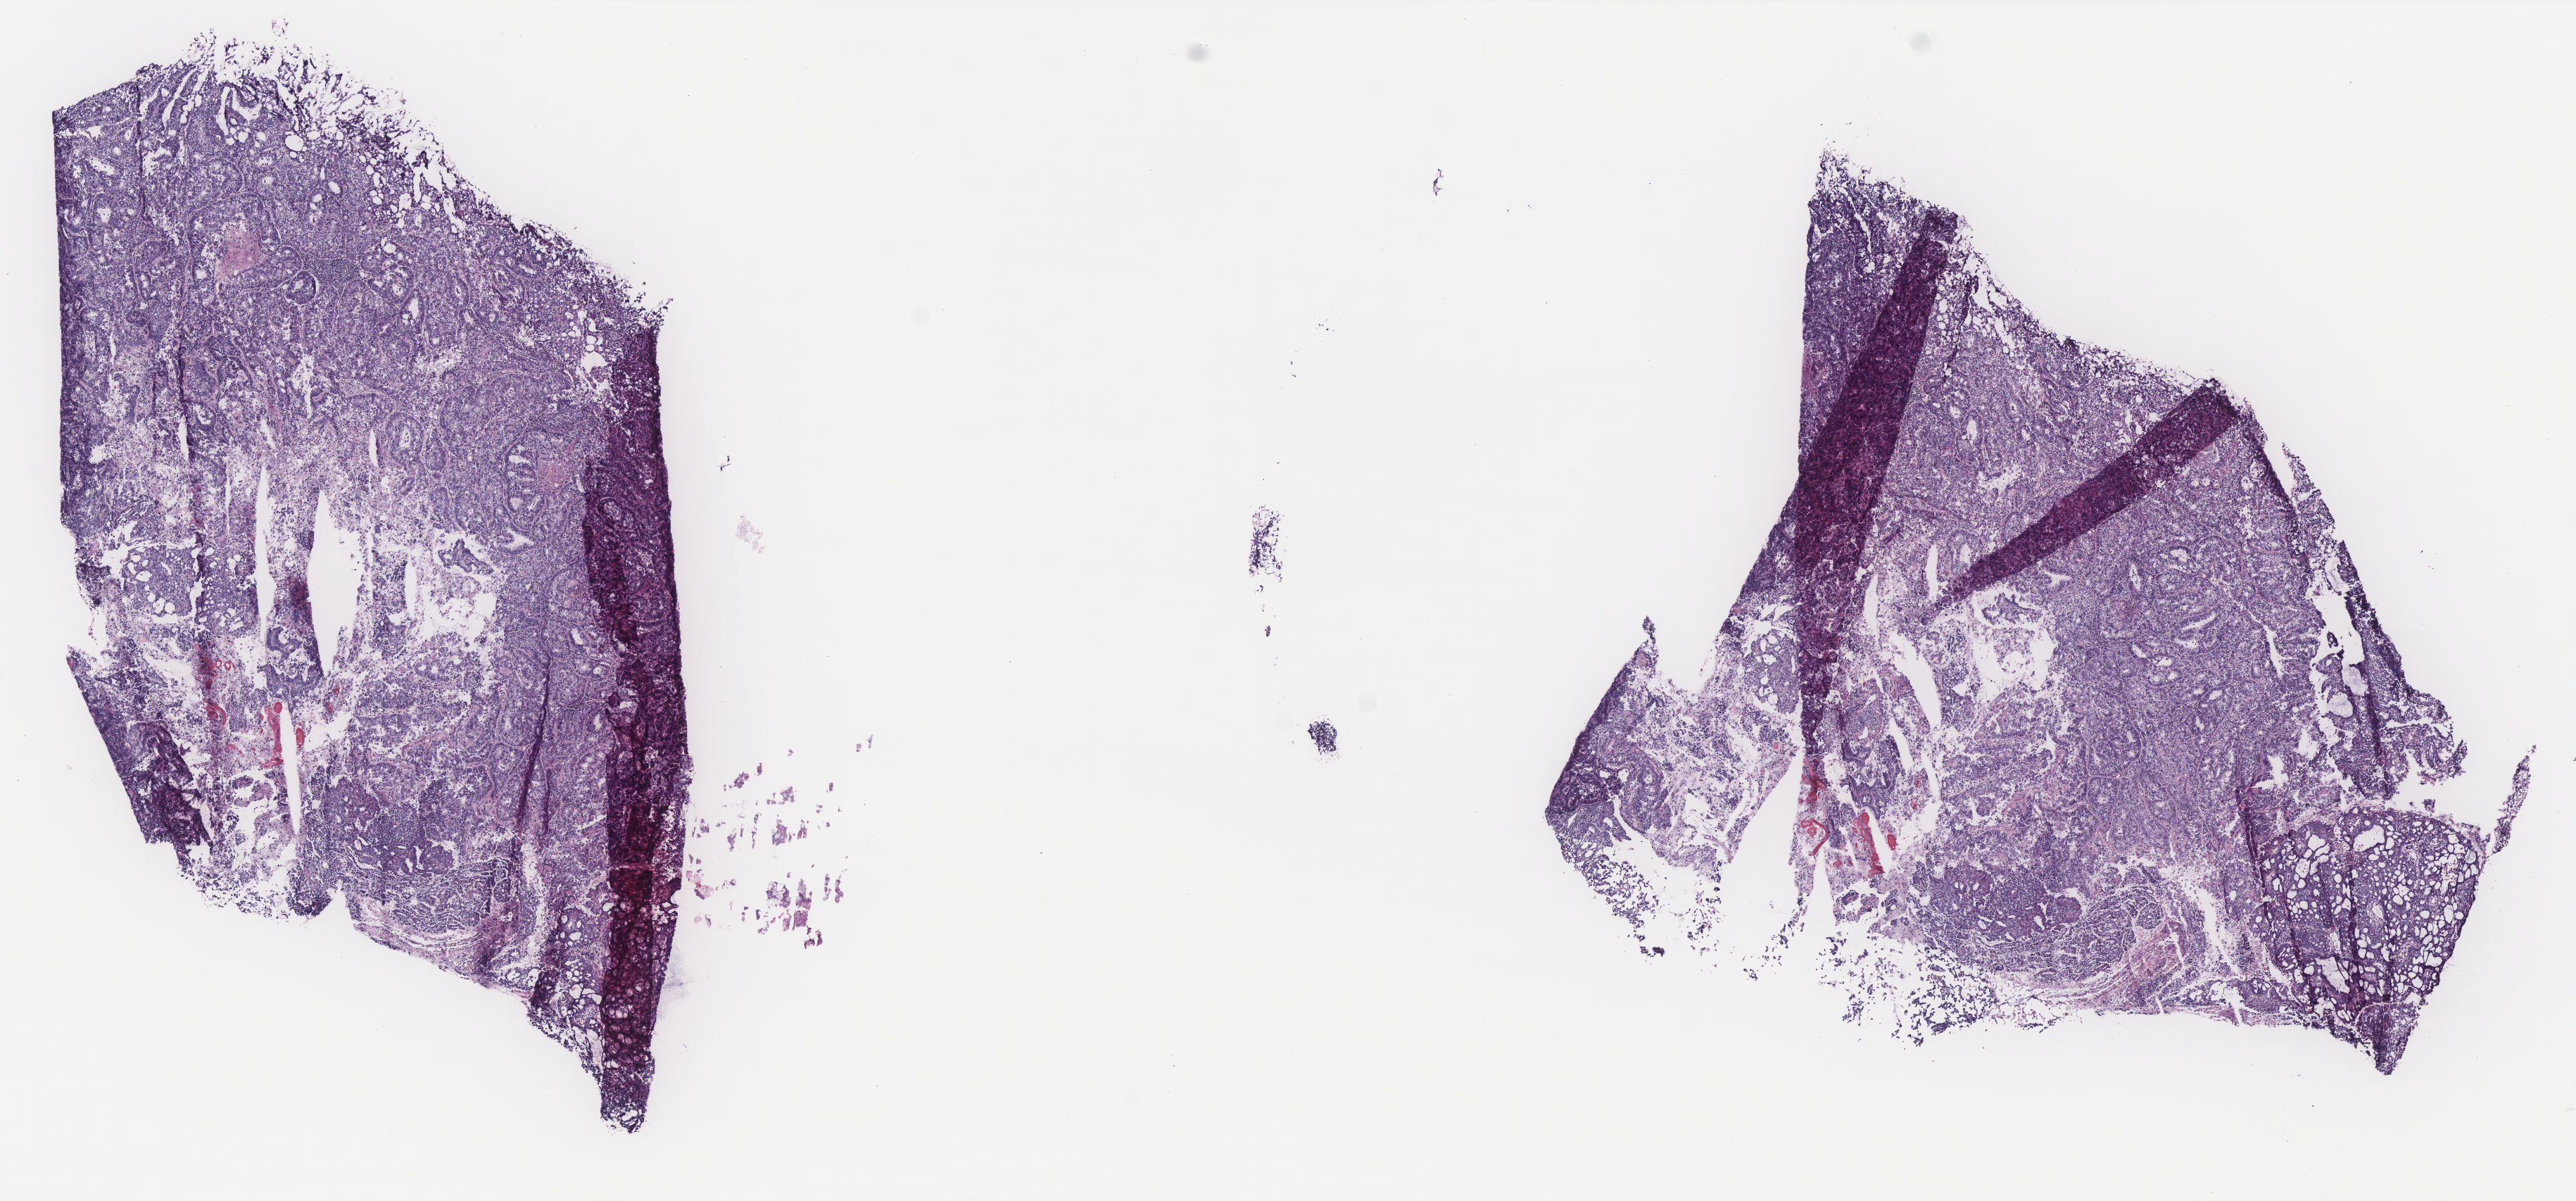
Whole-slide histology image, H&E-stained — whole scanned area (about 14.7 x 6.8 mm, acquisition: 40x scan) shown as a low-resolution overview. Frozen section from the top of the tissue portion. Sample: primary tumour, uterus. Female patient; age at initial diagnosis 74 years. Histologic grade: G3 (poorly differentiated). Pathologist review of this section (percent, as recorded): tumour cells 80%, tumour nuclei 100%, normal cells 0%, stromal cells 0%, necrosis 20%. Inflammatory infiltration, as recorded: lymphocyte infiltration 20%, monocyte infiltration 0%, neutrophil infiltration 20%.
FIGO stage: IA. Histologic diagnosis: Endometrioid adenocarcinoma, NOS (endometrium).